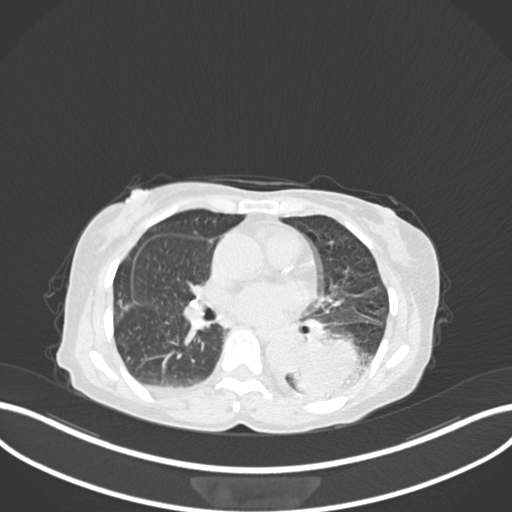
Chest CT, one axial slice. Slice 79 of 233 in the series (ordered by position). 120 kVp. Lung window (W 1500 / L -600 HU). 1 mm slice thickness. 512 × 512 image matrix, field of view 400 × 400 mm. Female patient, age 78 years. Case-level facts recorded for this patient, not image findings: clinical TNM (as recorded): T3 N0 M1.
Structures marked on this image (bounding box drawn by a radiologist):
- lung tumour (recorded histology: squamous cell carcinoma): box from (x=293, y=326) to (x=366, y=394) px